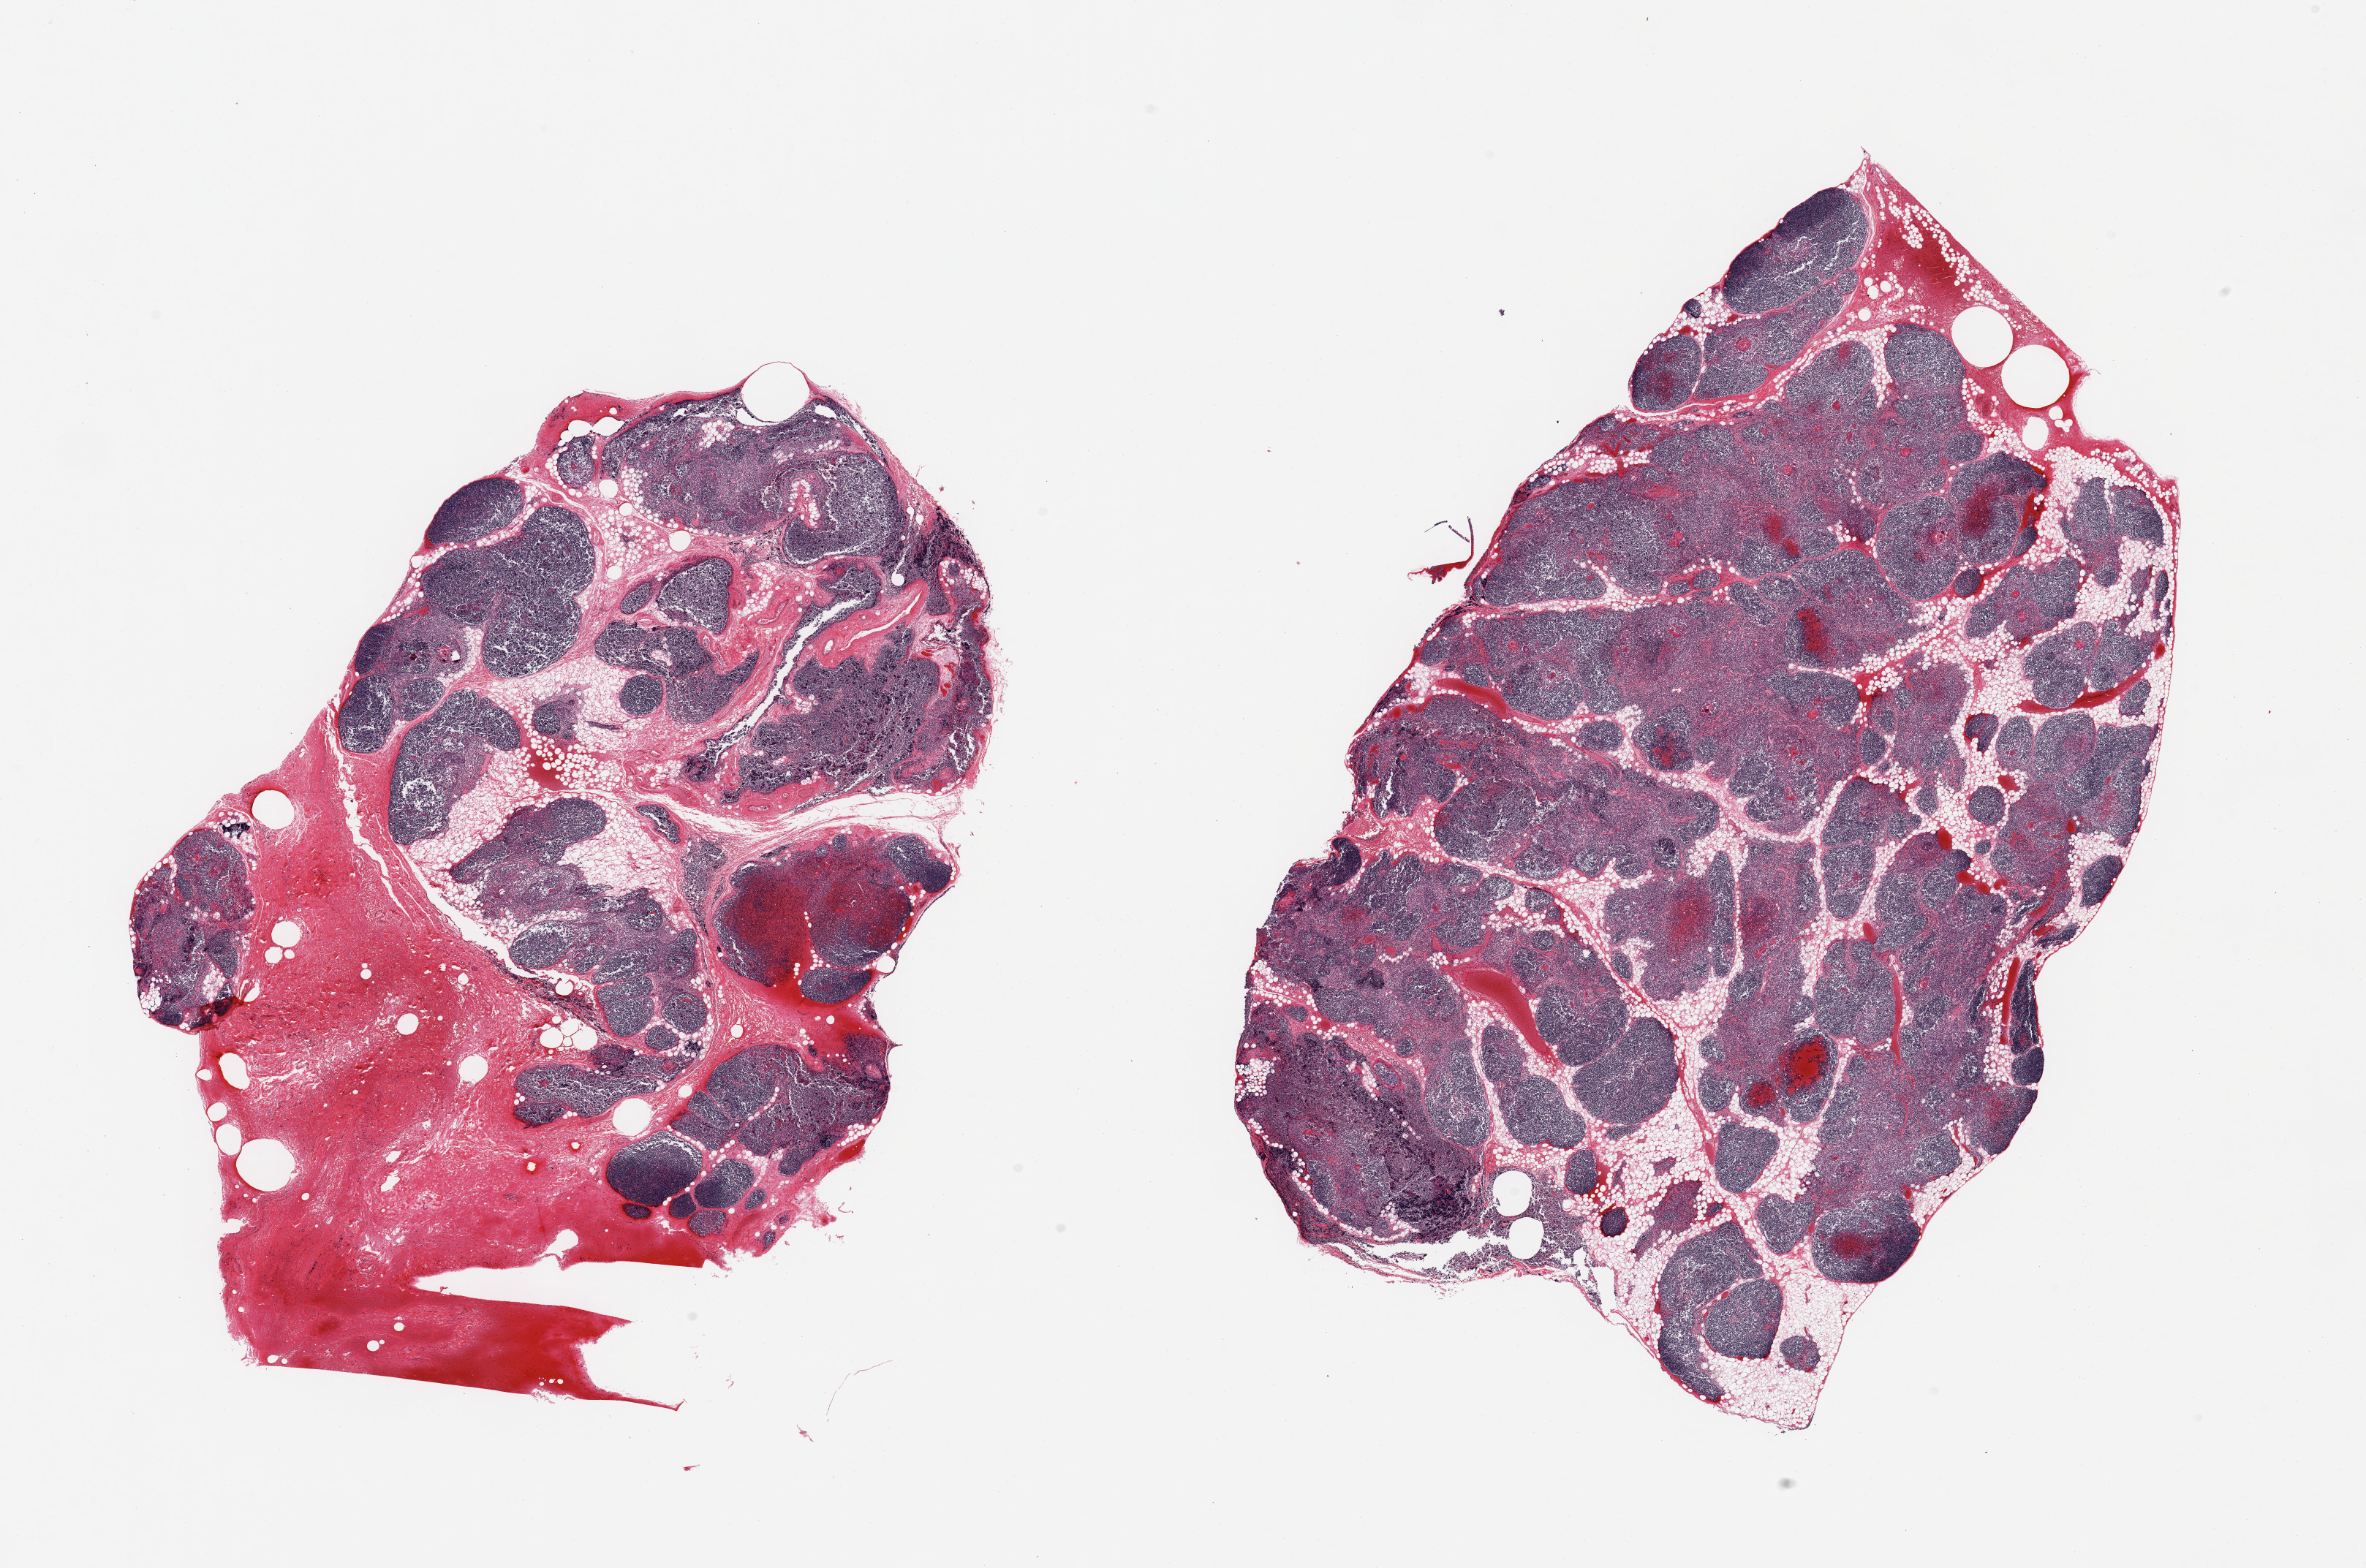
Hematoxylin and eosin (H&E) whole-slide image, shown as a low-resolution overview of the whole scanned area (about 25.6 x 17.0 mm); PAXgene-fixed paraffin-embedded (PFPE) section; section of thyroid (target tissue); tissue donor sample. Female donor.
* pathologist's review note for this sample: 2 pieces; thymus, not thyroid